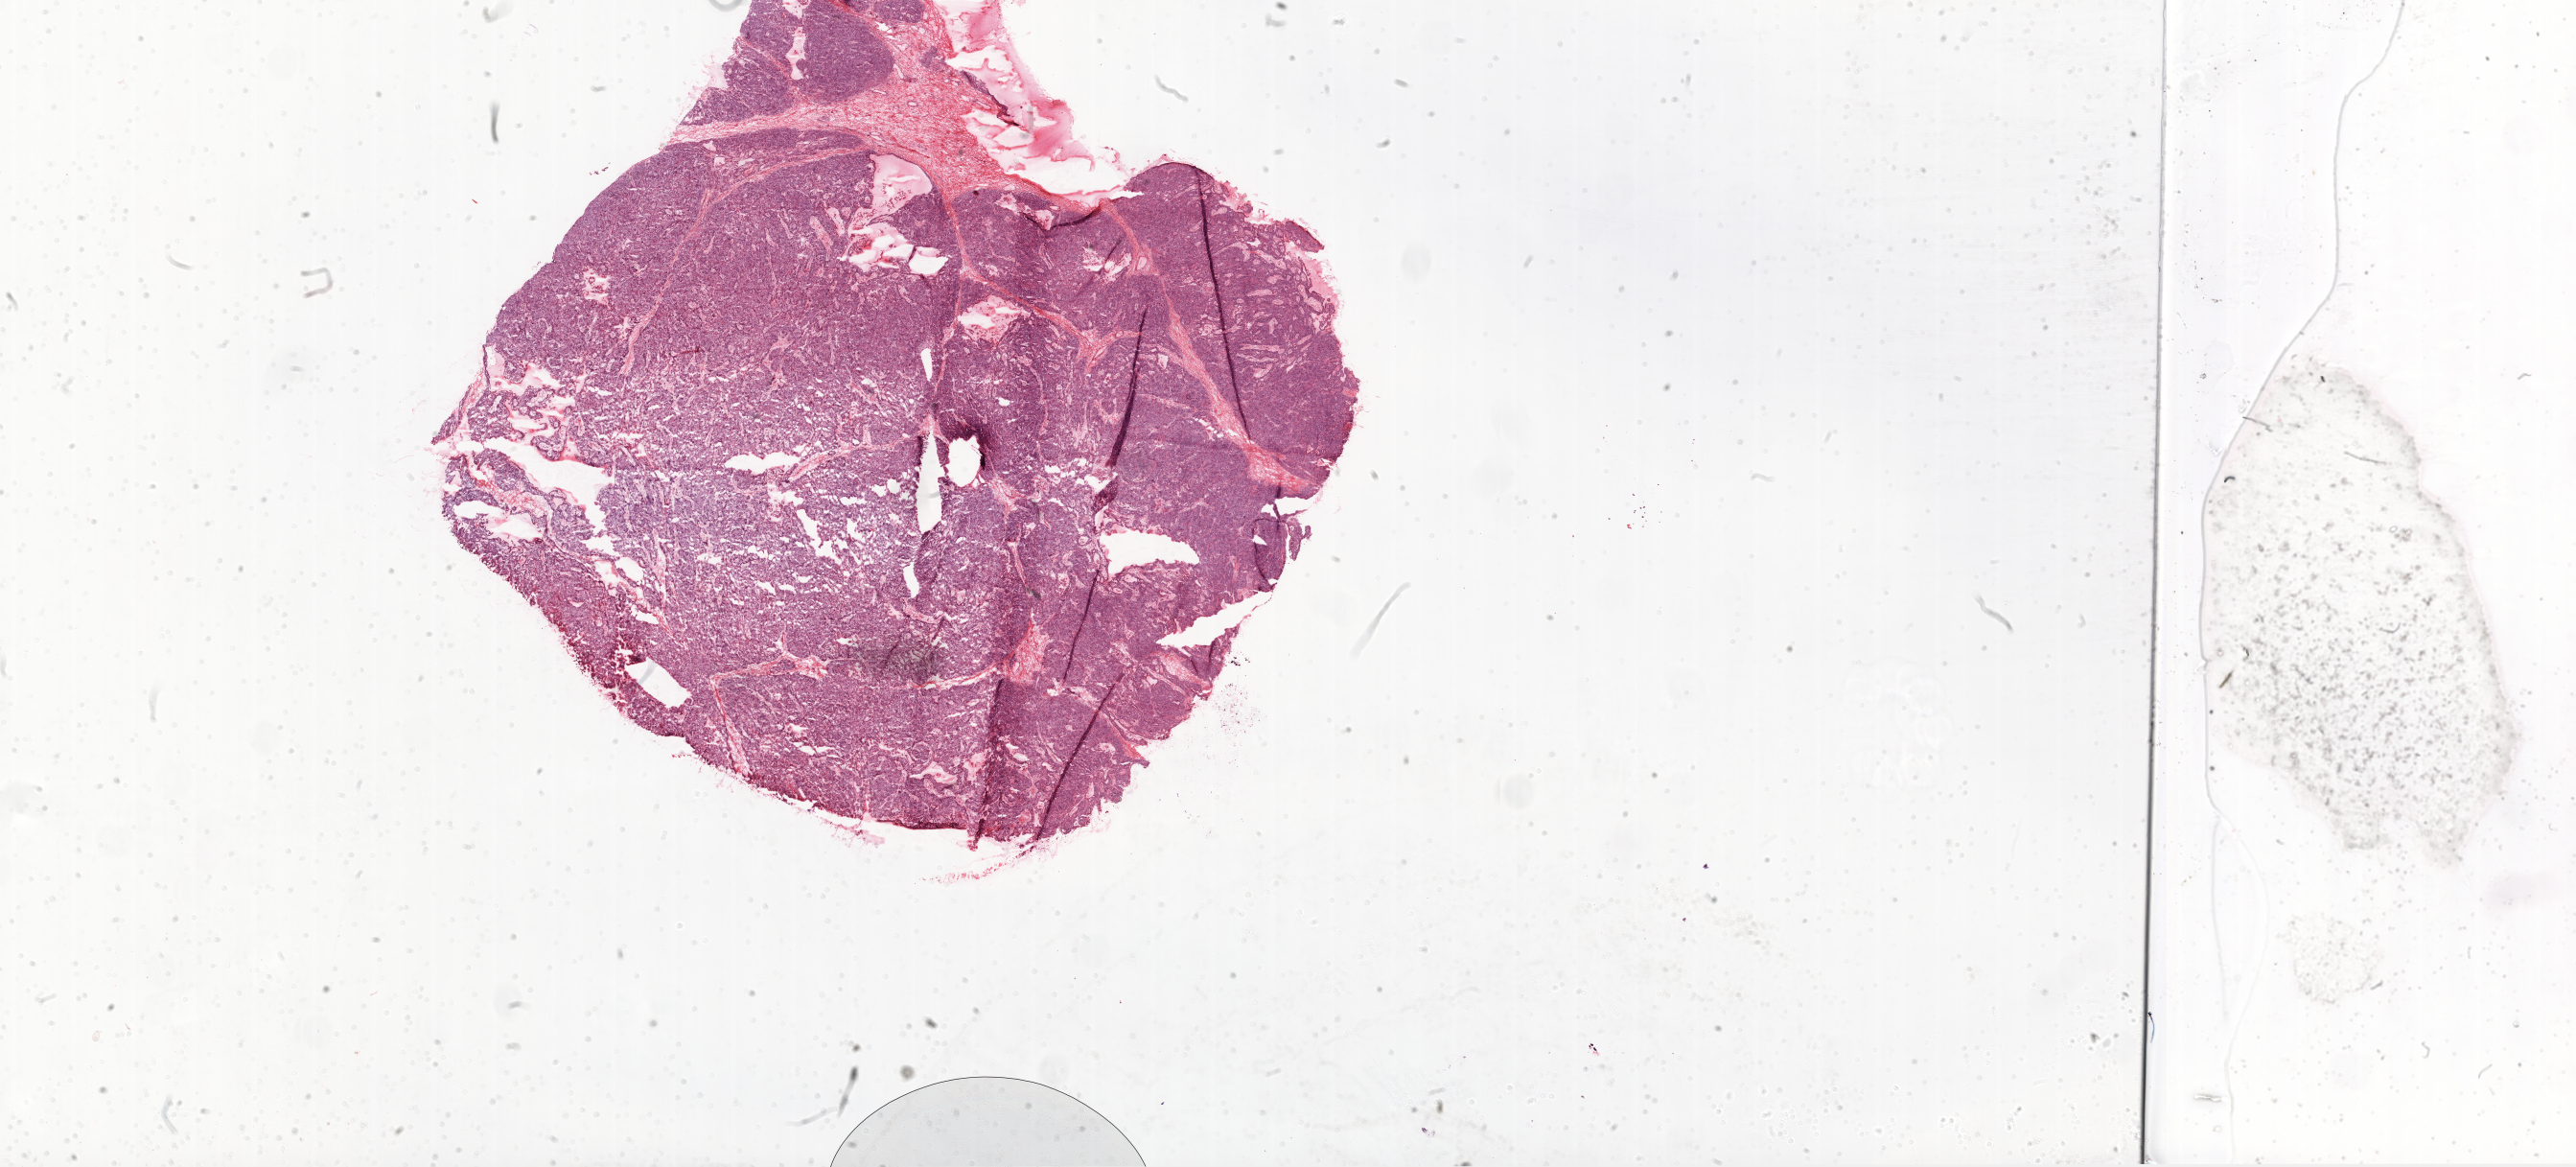
Digitized H&E-stained tissue section (whole slide), low-resolution overview of the scanned area, about 43.1 x 19.5 mm (from a 20x scan), frozen section, ovary, primary tumour sample. Patient: female, age at initial diagnosis 43 years. Histologic grade: G3 (poorly differentiated). Composition of this section per pathologist review: tumour cells 68%, tumour nuclei 75%, normal cells 10%, stromal cells 10%, necrosis 12%.
* FIGO stage: IIIC
* diagnosis: Serous cystadenocarcinoma, NOS